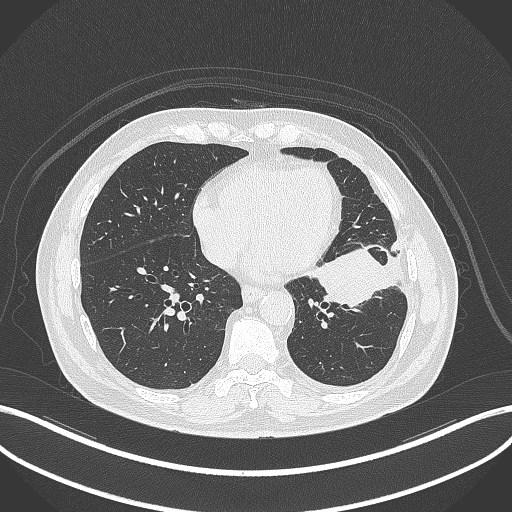
Chest CT, one axial slice; position 129 of 230 along the scan axis; 120 kVp; lung window (W 1500 / L -600 HU); 1 mm slice thickness; 512 × 512 image matrix, field of view 400 × 400 mm. Male patient, age 68 years. From the clinical record (not read from this slice): clinical TNM (as recorded): T2b N0 M0.
Structures marked on this image (bounding box drawn by a radiologist):
- lung tumour (recorded histology: squamous cell carcinoma): bounding box <313,247,404,310> (left, top, right, bottom; pixels)